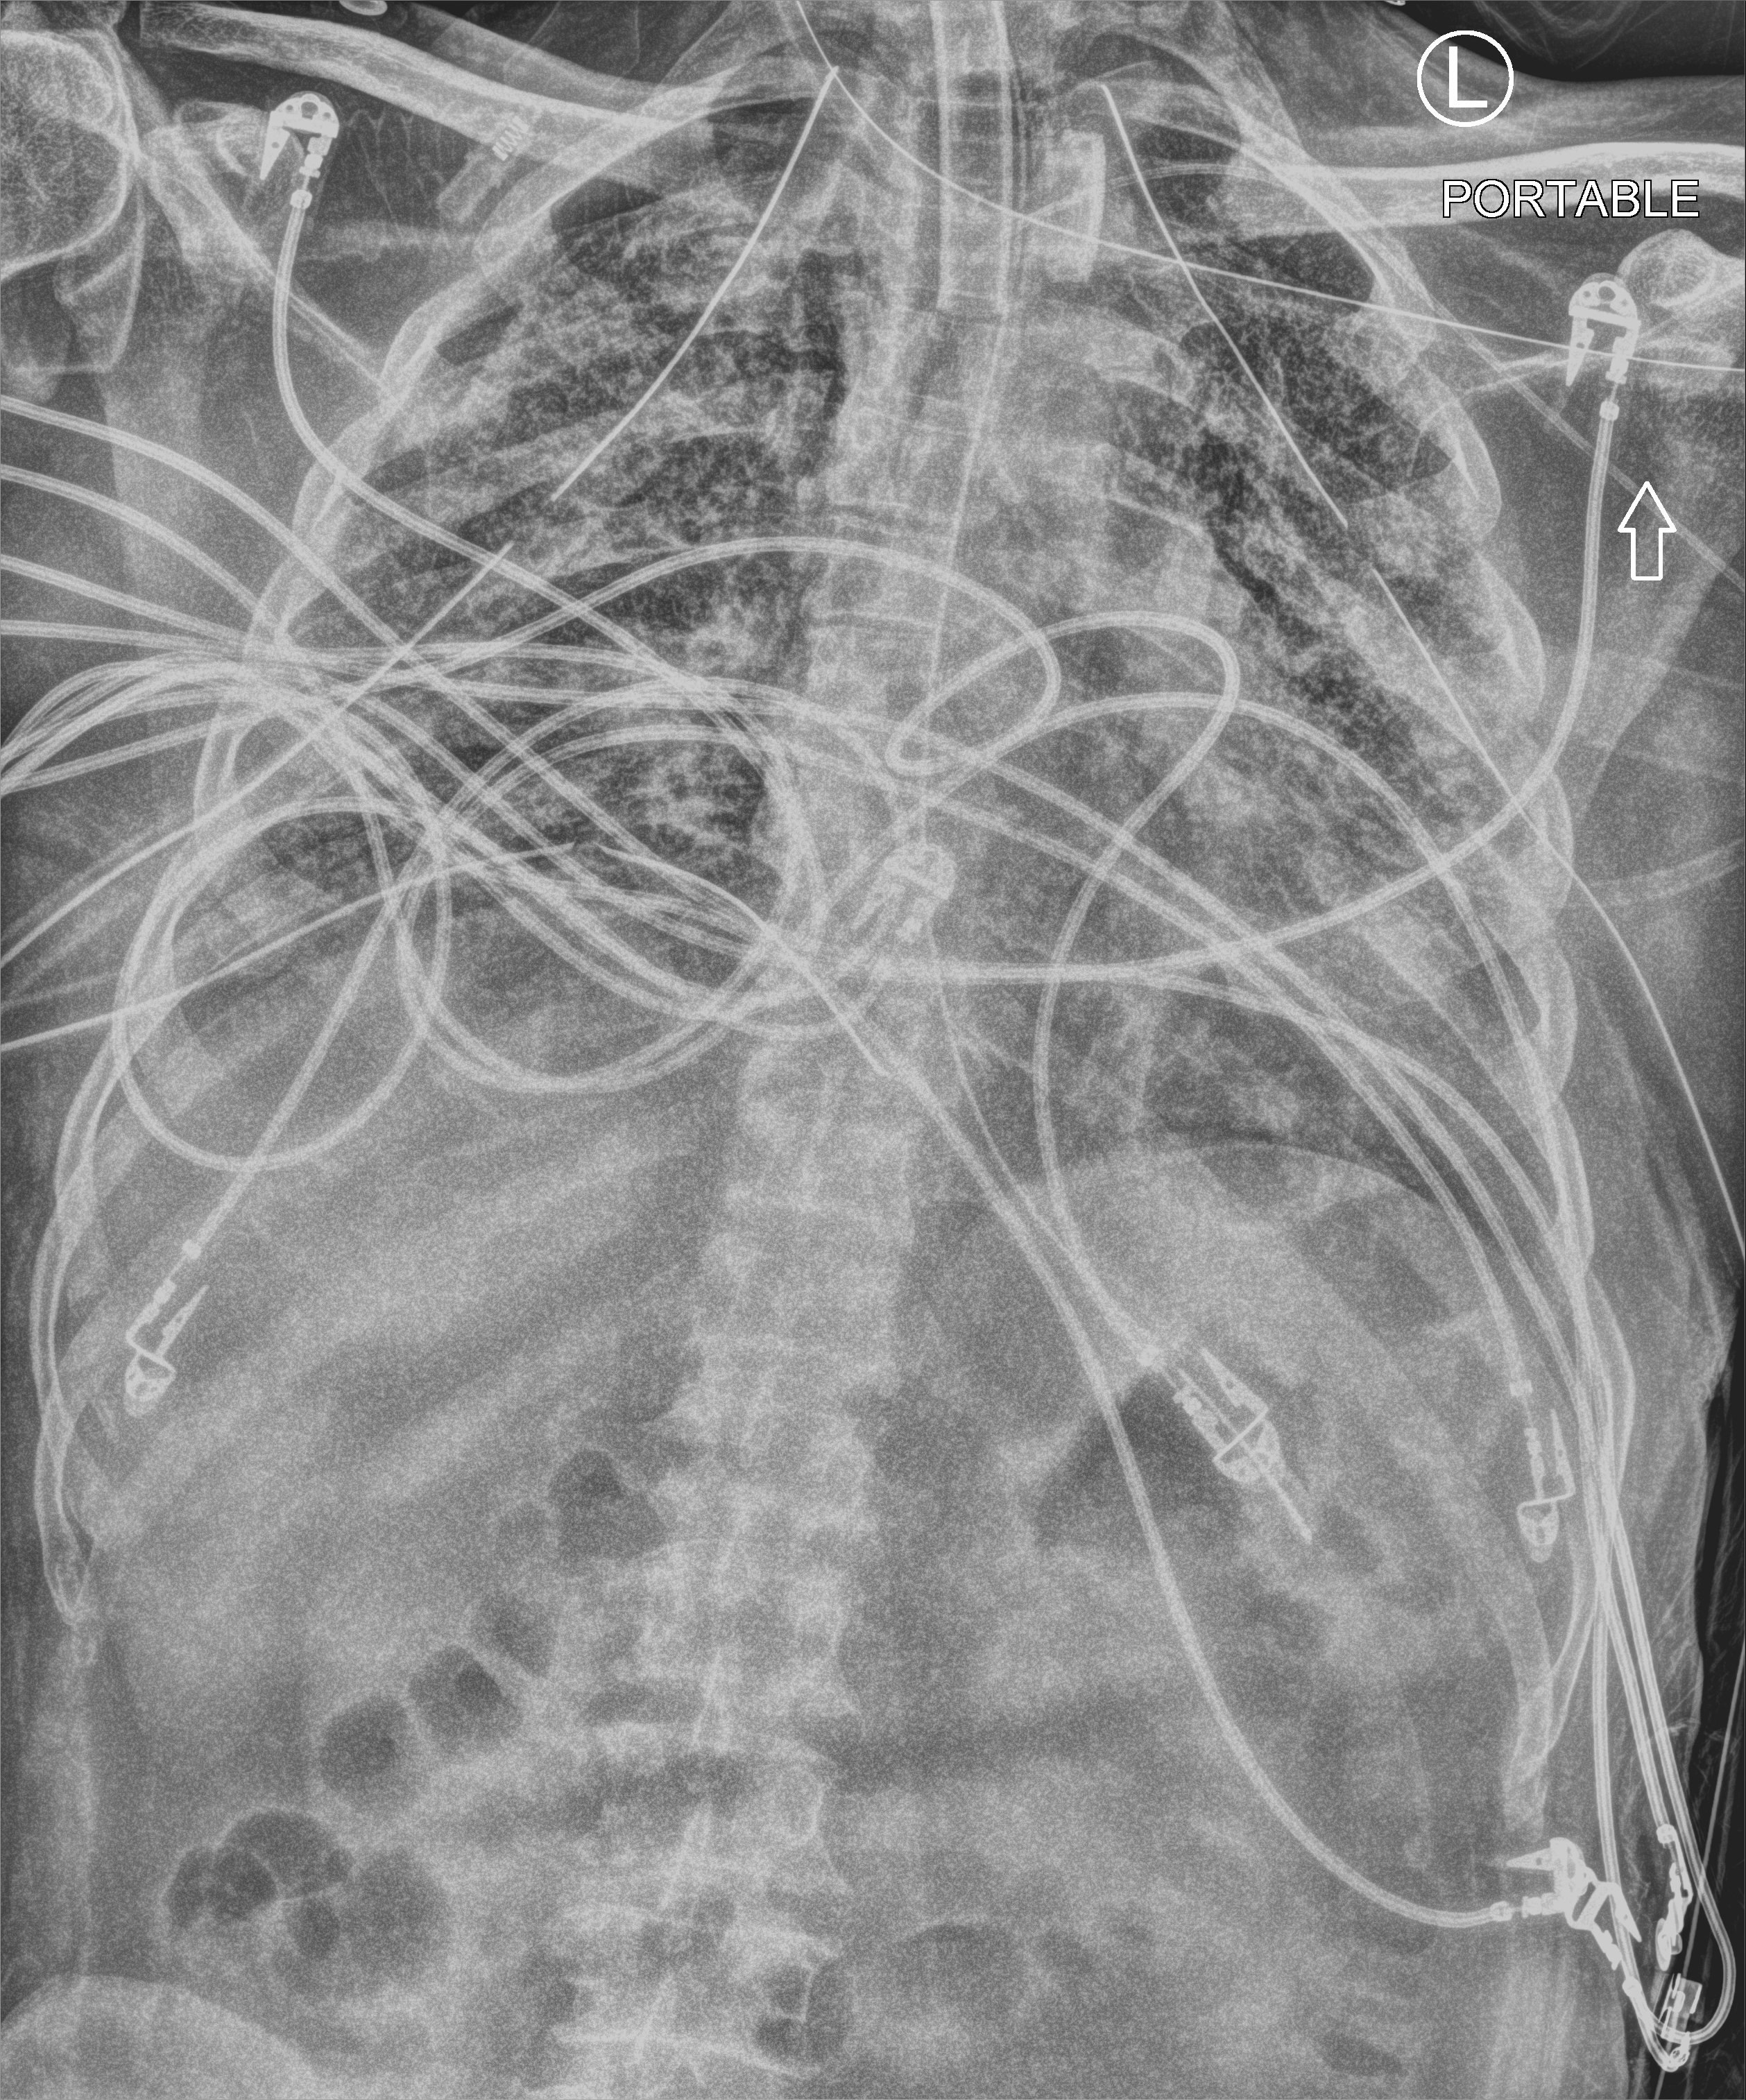
Bedside chest radiograph (computed radiography); anteroposterior (AP) projection. Patient hospitalised with COVID-19; male, aged 18–59 years.
Hospital-stay facts (about this admission, not read from this image; timing relative to this image not recorded): mechanically ventilated during this hospital stay: yes.